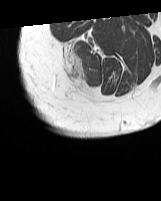
MRI of an extremity soft-tissue mass, one axial slice; position 9 of 70 along the scan axis; MR volume resampled by the dataset authors to the PET/CT grid (not the native acquisition matrix); 161 × 201 image matrix. Female patient. From the clinical record (not read from this slice): histological type: synovial sarcoma; grade: intermediate; site of the primary tumour: right buttock.
Annotated regions visible in this slice (expert contour drawn on MRI and transferred to this co-registered scan by the dataset authors):
- gross tumour volume including surrounding oedema: bounding box (x1, y1, x2, y2) in pixels: (63, 43, 84, 85)